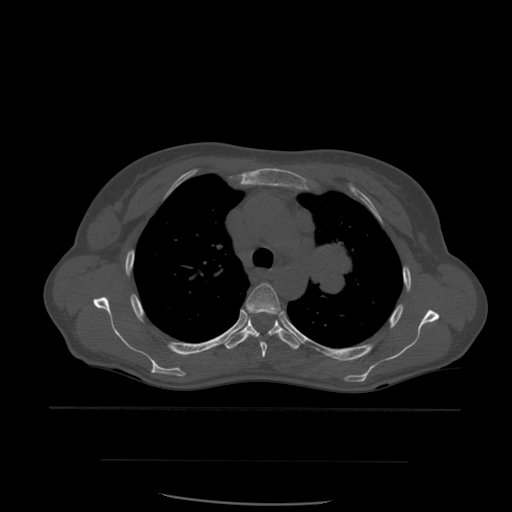
CT including the spine, one axial slice. Position 418 of 574 along the scan axis. Bone window (W 1800 / L 400 HU). 1.25 mm slice thickness. 512 × 512 image matrix, field of view 392 × 392 mm. Patient age 48 years. Case-level facts recorded for this patient, not image findings: primary cancer: lung.
Structures marked on this image (semi-automatically segmented with operator editing):
- T4 vertebra: bounding box <244,283,282,359> (left, top, right, bottom; pixels)
- T5 vertebra: <225,312,300,350>